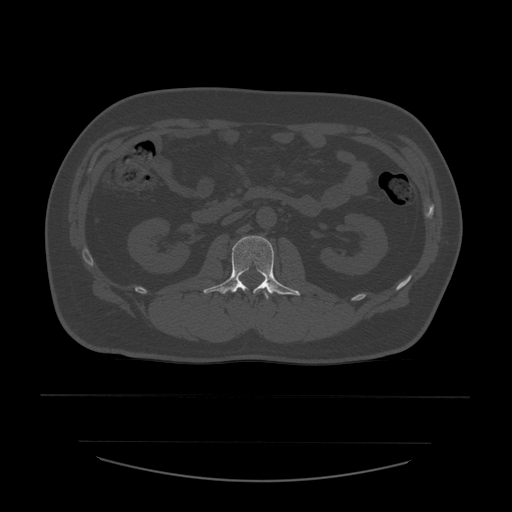
CT including the spine, one axial slice; position 203 of 532 along the scan axis; 120 kVp; bone window (W 1800 / L 400 HU); 512 × 512 image matrix. Patient age 44 years. From the clinical record (not read from this slice): primary cancer: soft tissue sarcoma.
Annotated regions visible in this slice (semi-automatically segmented with operator editing):
- L1 vertebra: bounding box <264,291,270,300> (left, top, right, bottom; pixels)
- L2 vertebra: <204,236,300,296>